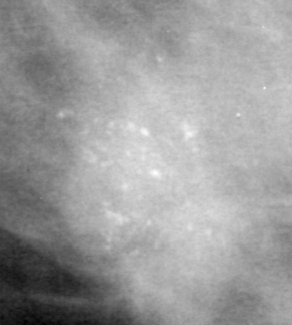
Region of interest cut from a scanned film mammogram (one marked finding); right breast; MLO view; BI-RADS breast density category 4 (scale 1–4).
Calcifications, morphology pleomorphic, distribution clustered; BI-RADS assessment category 4; subtlety rating 3 on a 1 (subtle) to 5 (obvious) scale; pathology result (as recorded, not read from the image): malignant.